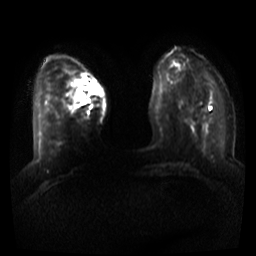
Breast MRI, one axial slice. Slice 11 of 44 in the series (ordered by position). Diffusion-weighted series; image 2 of 4 stored at this slice position (different b-values; order by instance number). 3 T. 5 mm slice thickness. 256 × 256 image matrix, field of view 340 × 340 mm. Female patient.
Structures marked on this image (outlined manually by an expert reader):
- tumour on diffusion-weighted imaging: bounding box (x1, y1, x2, y2) in pixels: (78, 95, 84, 101)